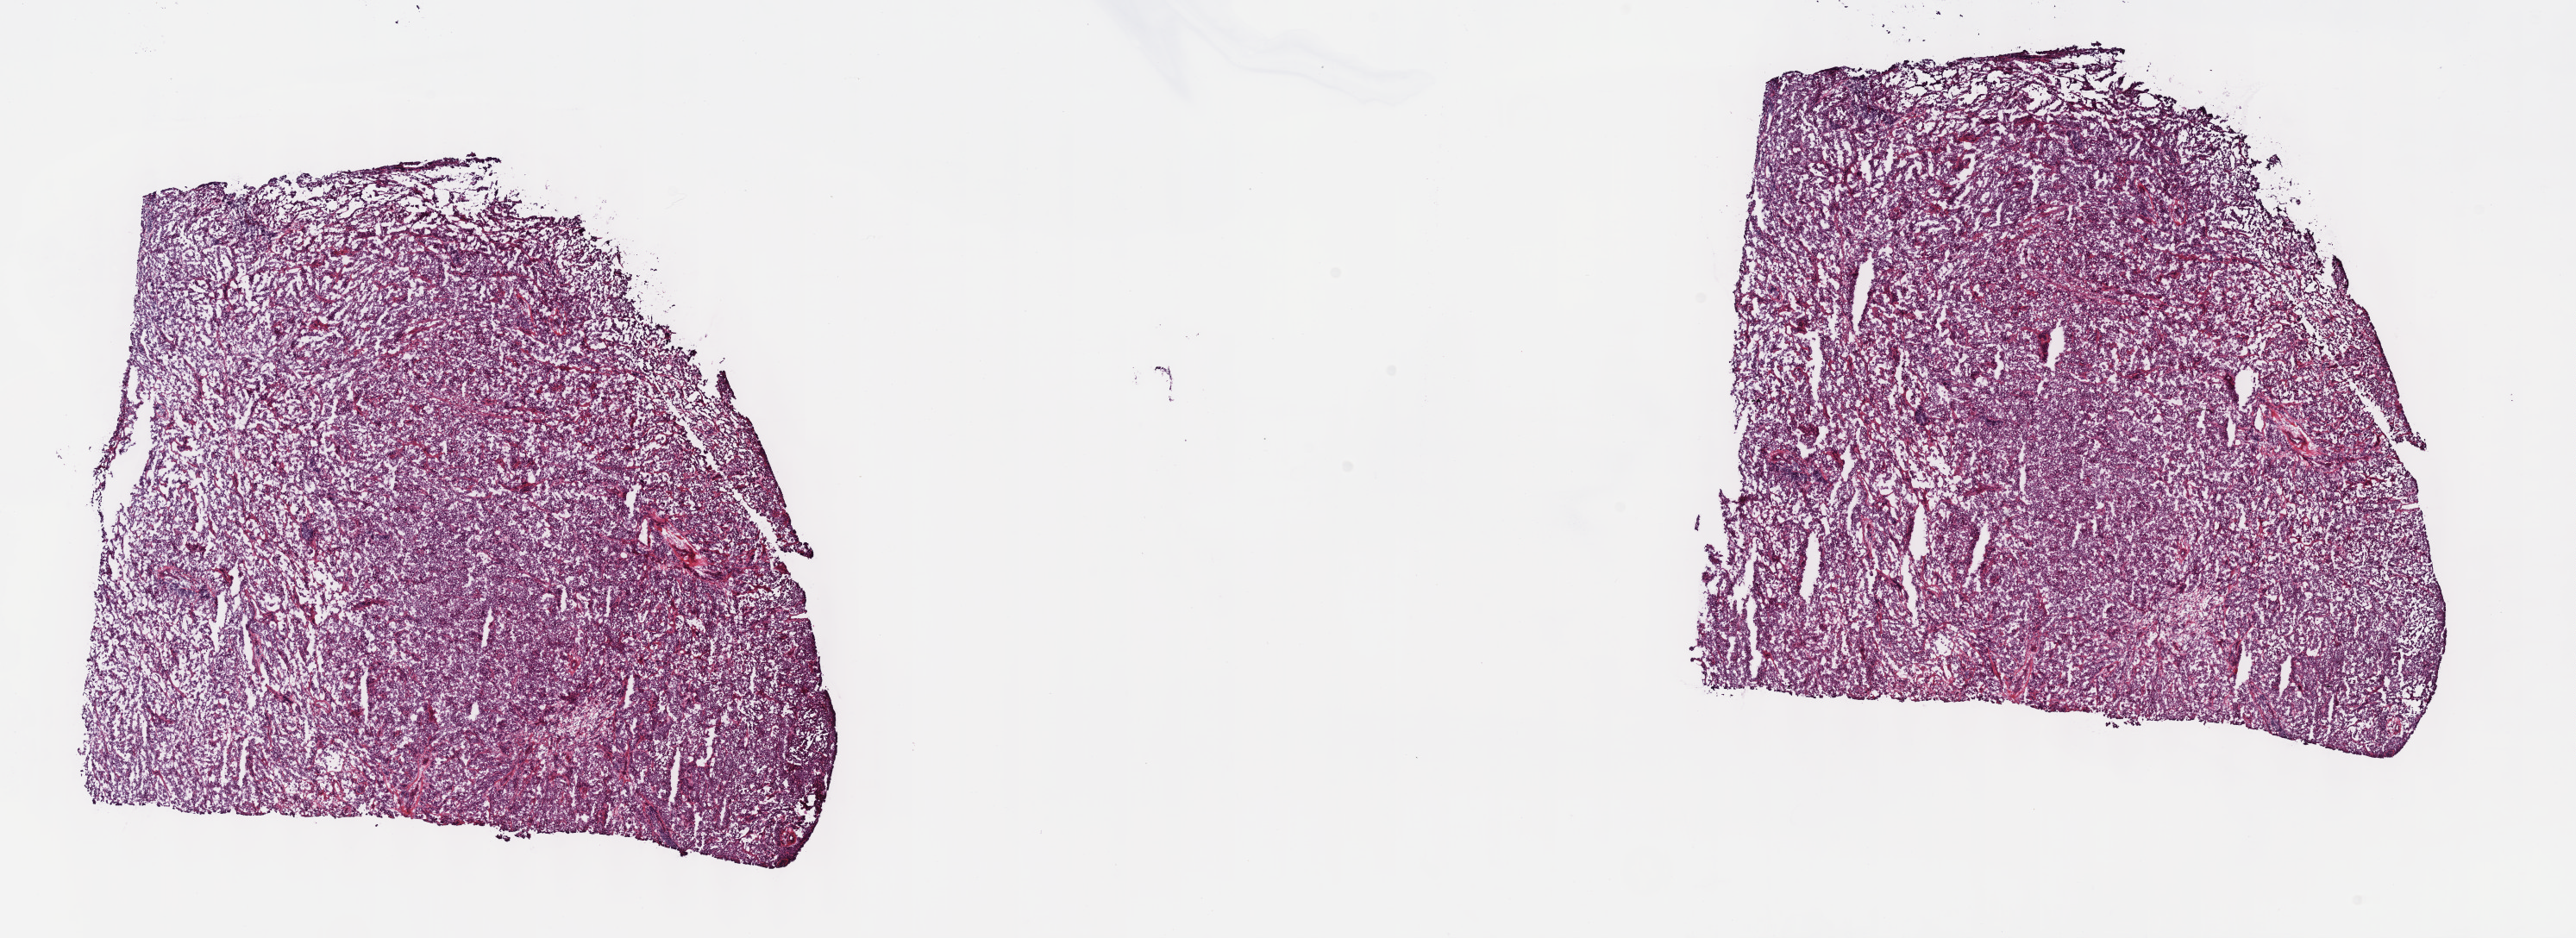
Digitized H&E tissue section (whole slide) — low-resolution overview of the scanned area, about 24.2 x 8.8 mm (acquisition: 40x scan); frozen section; metastatic tumour sample. Patient: male, age at initial diagnosis 48 years. Composition of this section per pathologist review: tumour cells 90%, tumour nuclei 95%, normal cells 0%, stromal cells 10%, necrosis 0%. Inflammatory infiltration, as recorded: lymphocyte infiltration 0%, monocyte infiltration 0%, neutrophil infiltration 0%.
* this section: metastatic tumour tissue
* patient diagnosis: Malignant melanoma, NOS